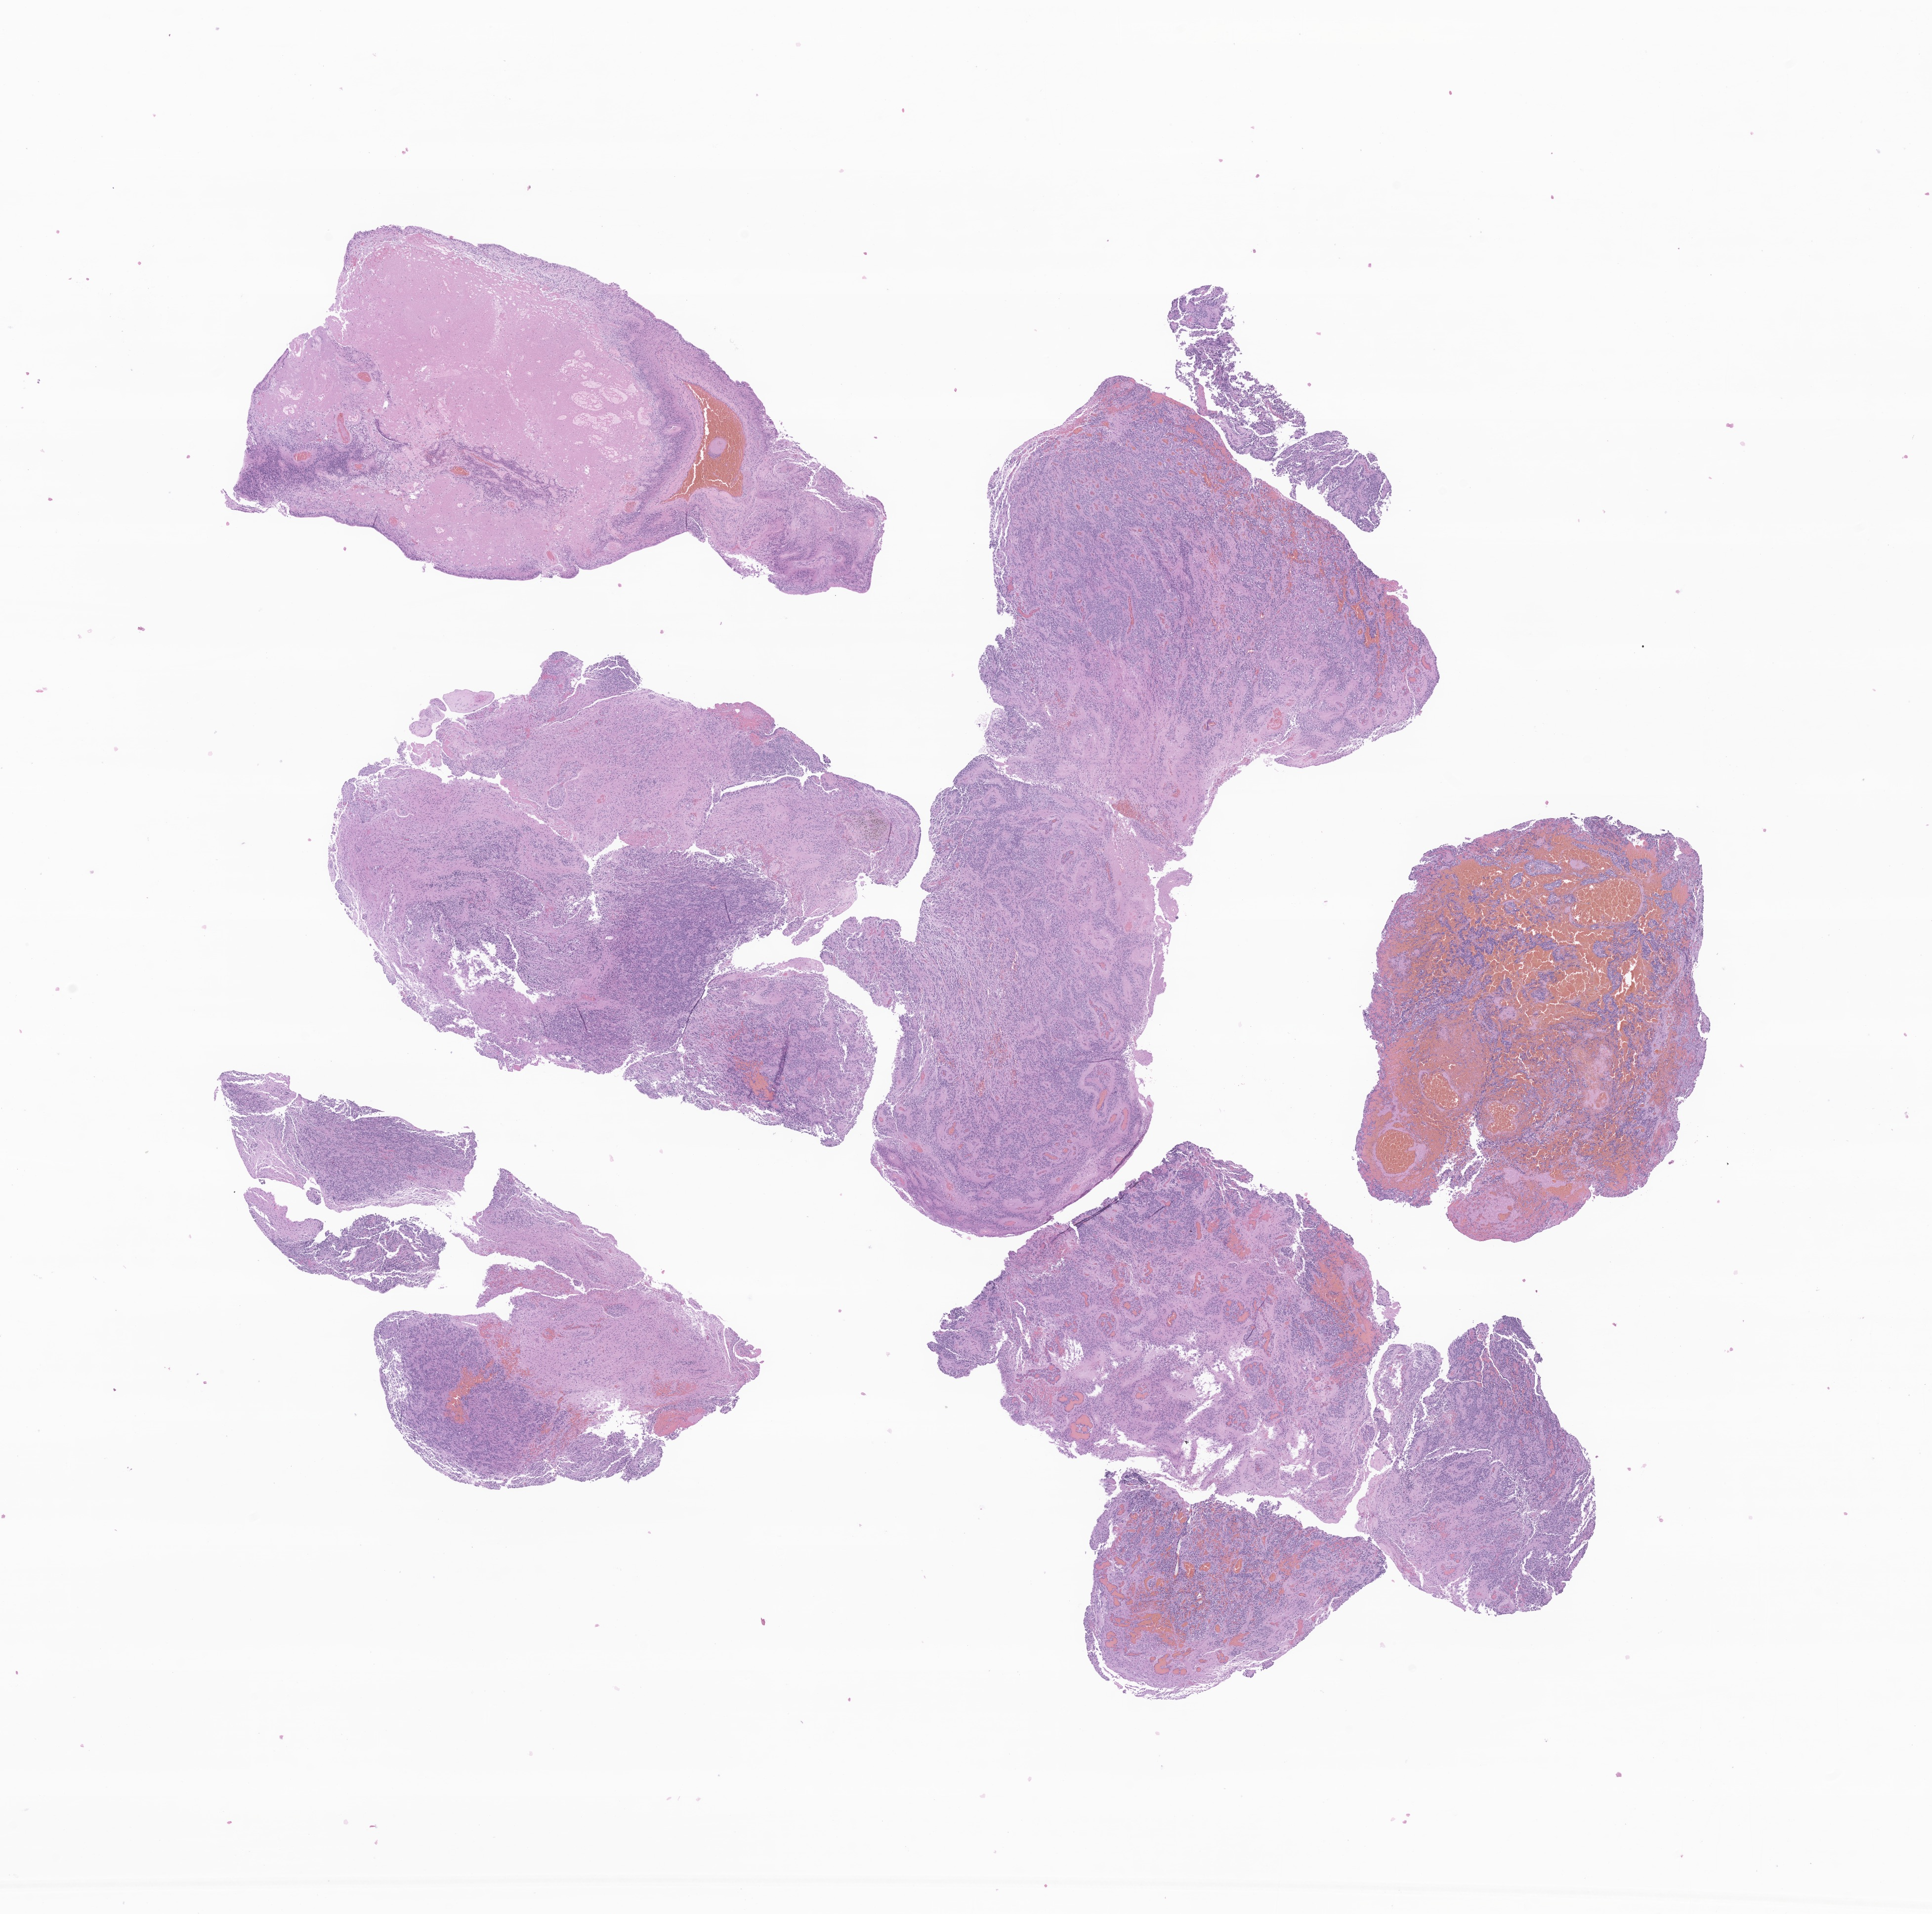
Whole-slide image, hematoxylin and eosin (H&E) stain of tumor tissue from the brain — a low-resolution overview of the entire scanned area, about 16.5 x 16.3 mm, formalin-fixed, paraffin-embedded (FFPE) tissue. Patient: female, age 60 months (5 years).
Diagnosis (ICD-O-3 morphology term): Ependymoma, NOS.